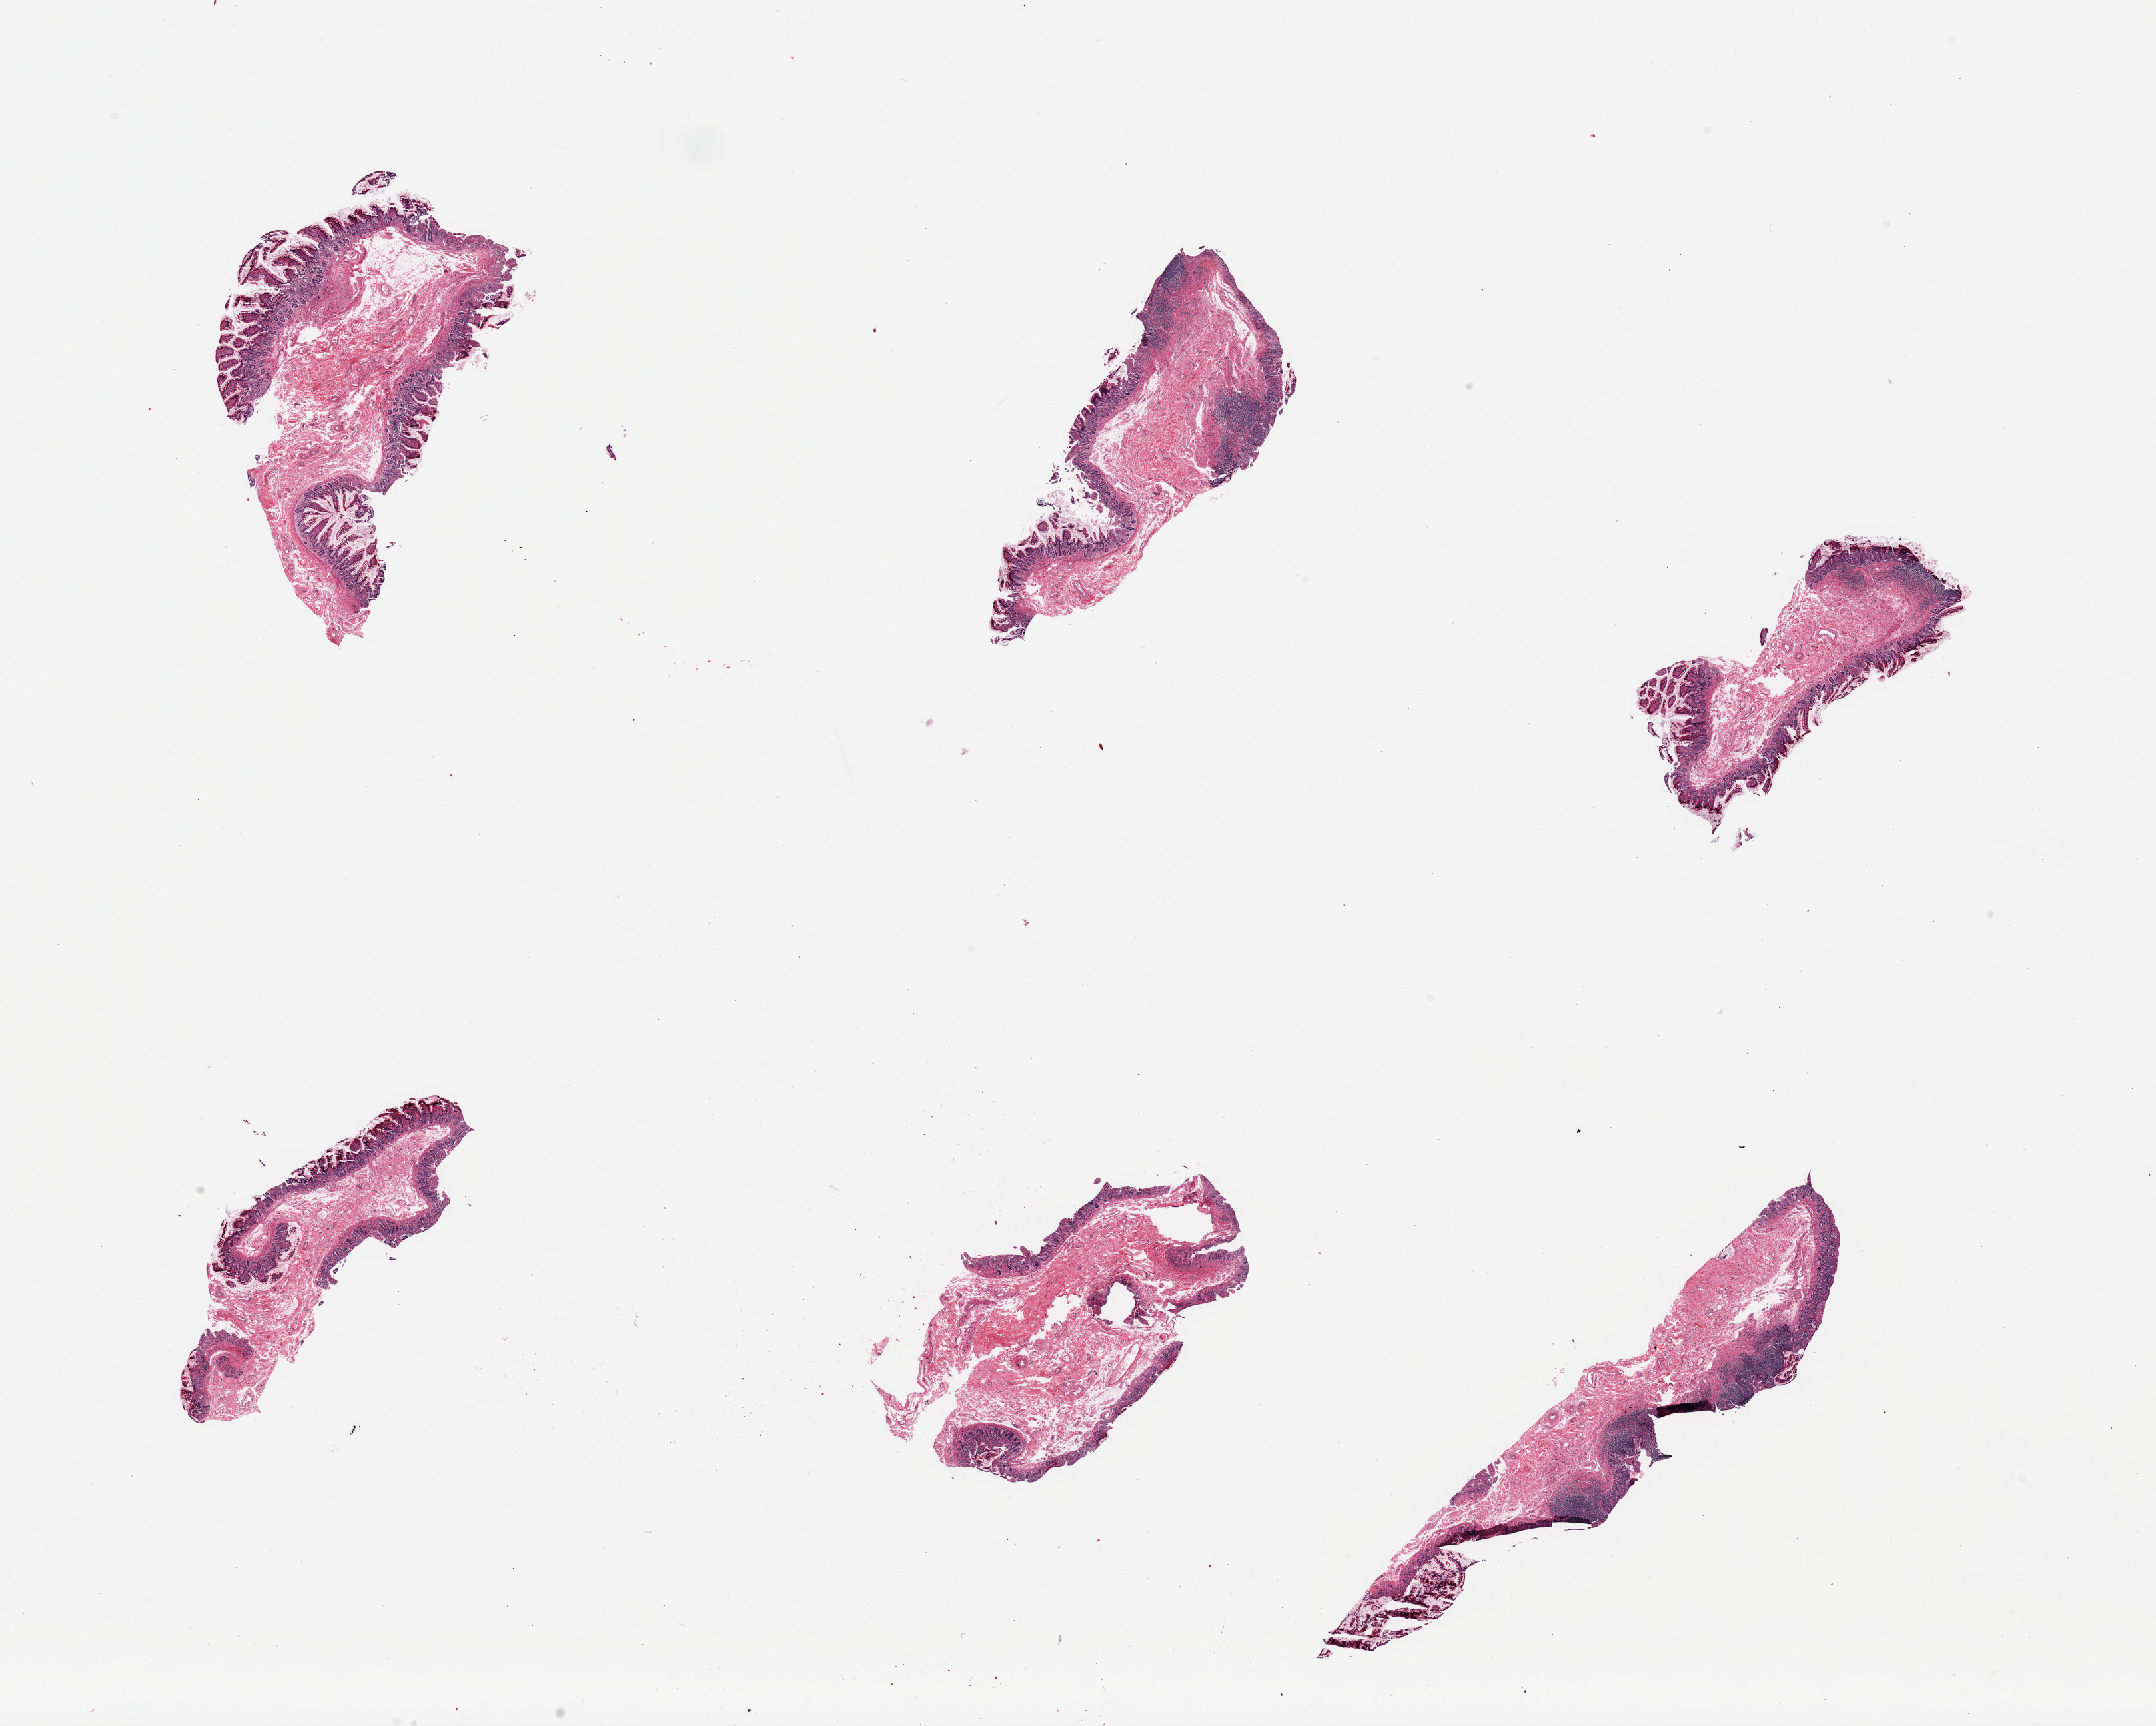
Whole-slide image, H&E stain — low-resolution overview of the scanned area, about 25.6 x 20.5 mm (slide scanned at 20x), PAXgene-fixed paraffin-embedded (PFPE) section, sampled site (target tissue): ileum, tissue donor sample.
Review note (as recorded): 6 pieces, target lymphoid aggregates are ~10% of tissue.